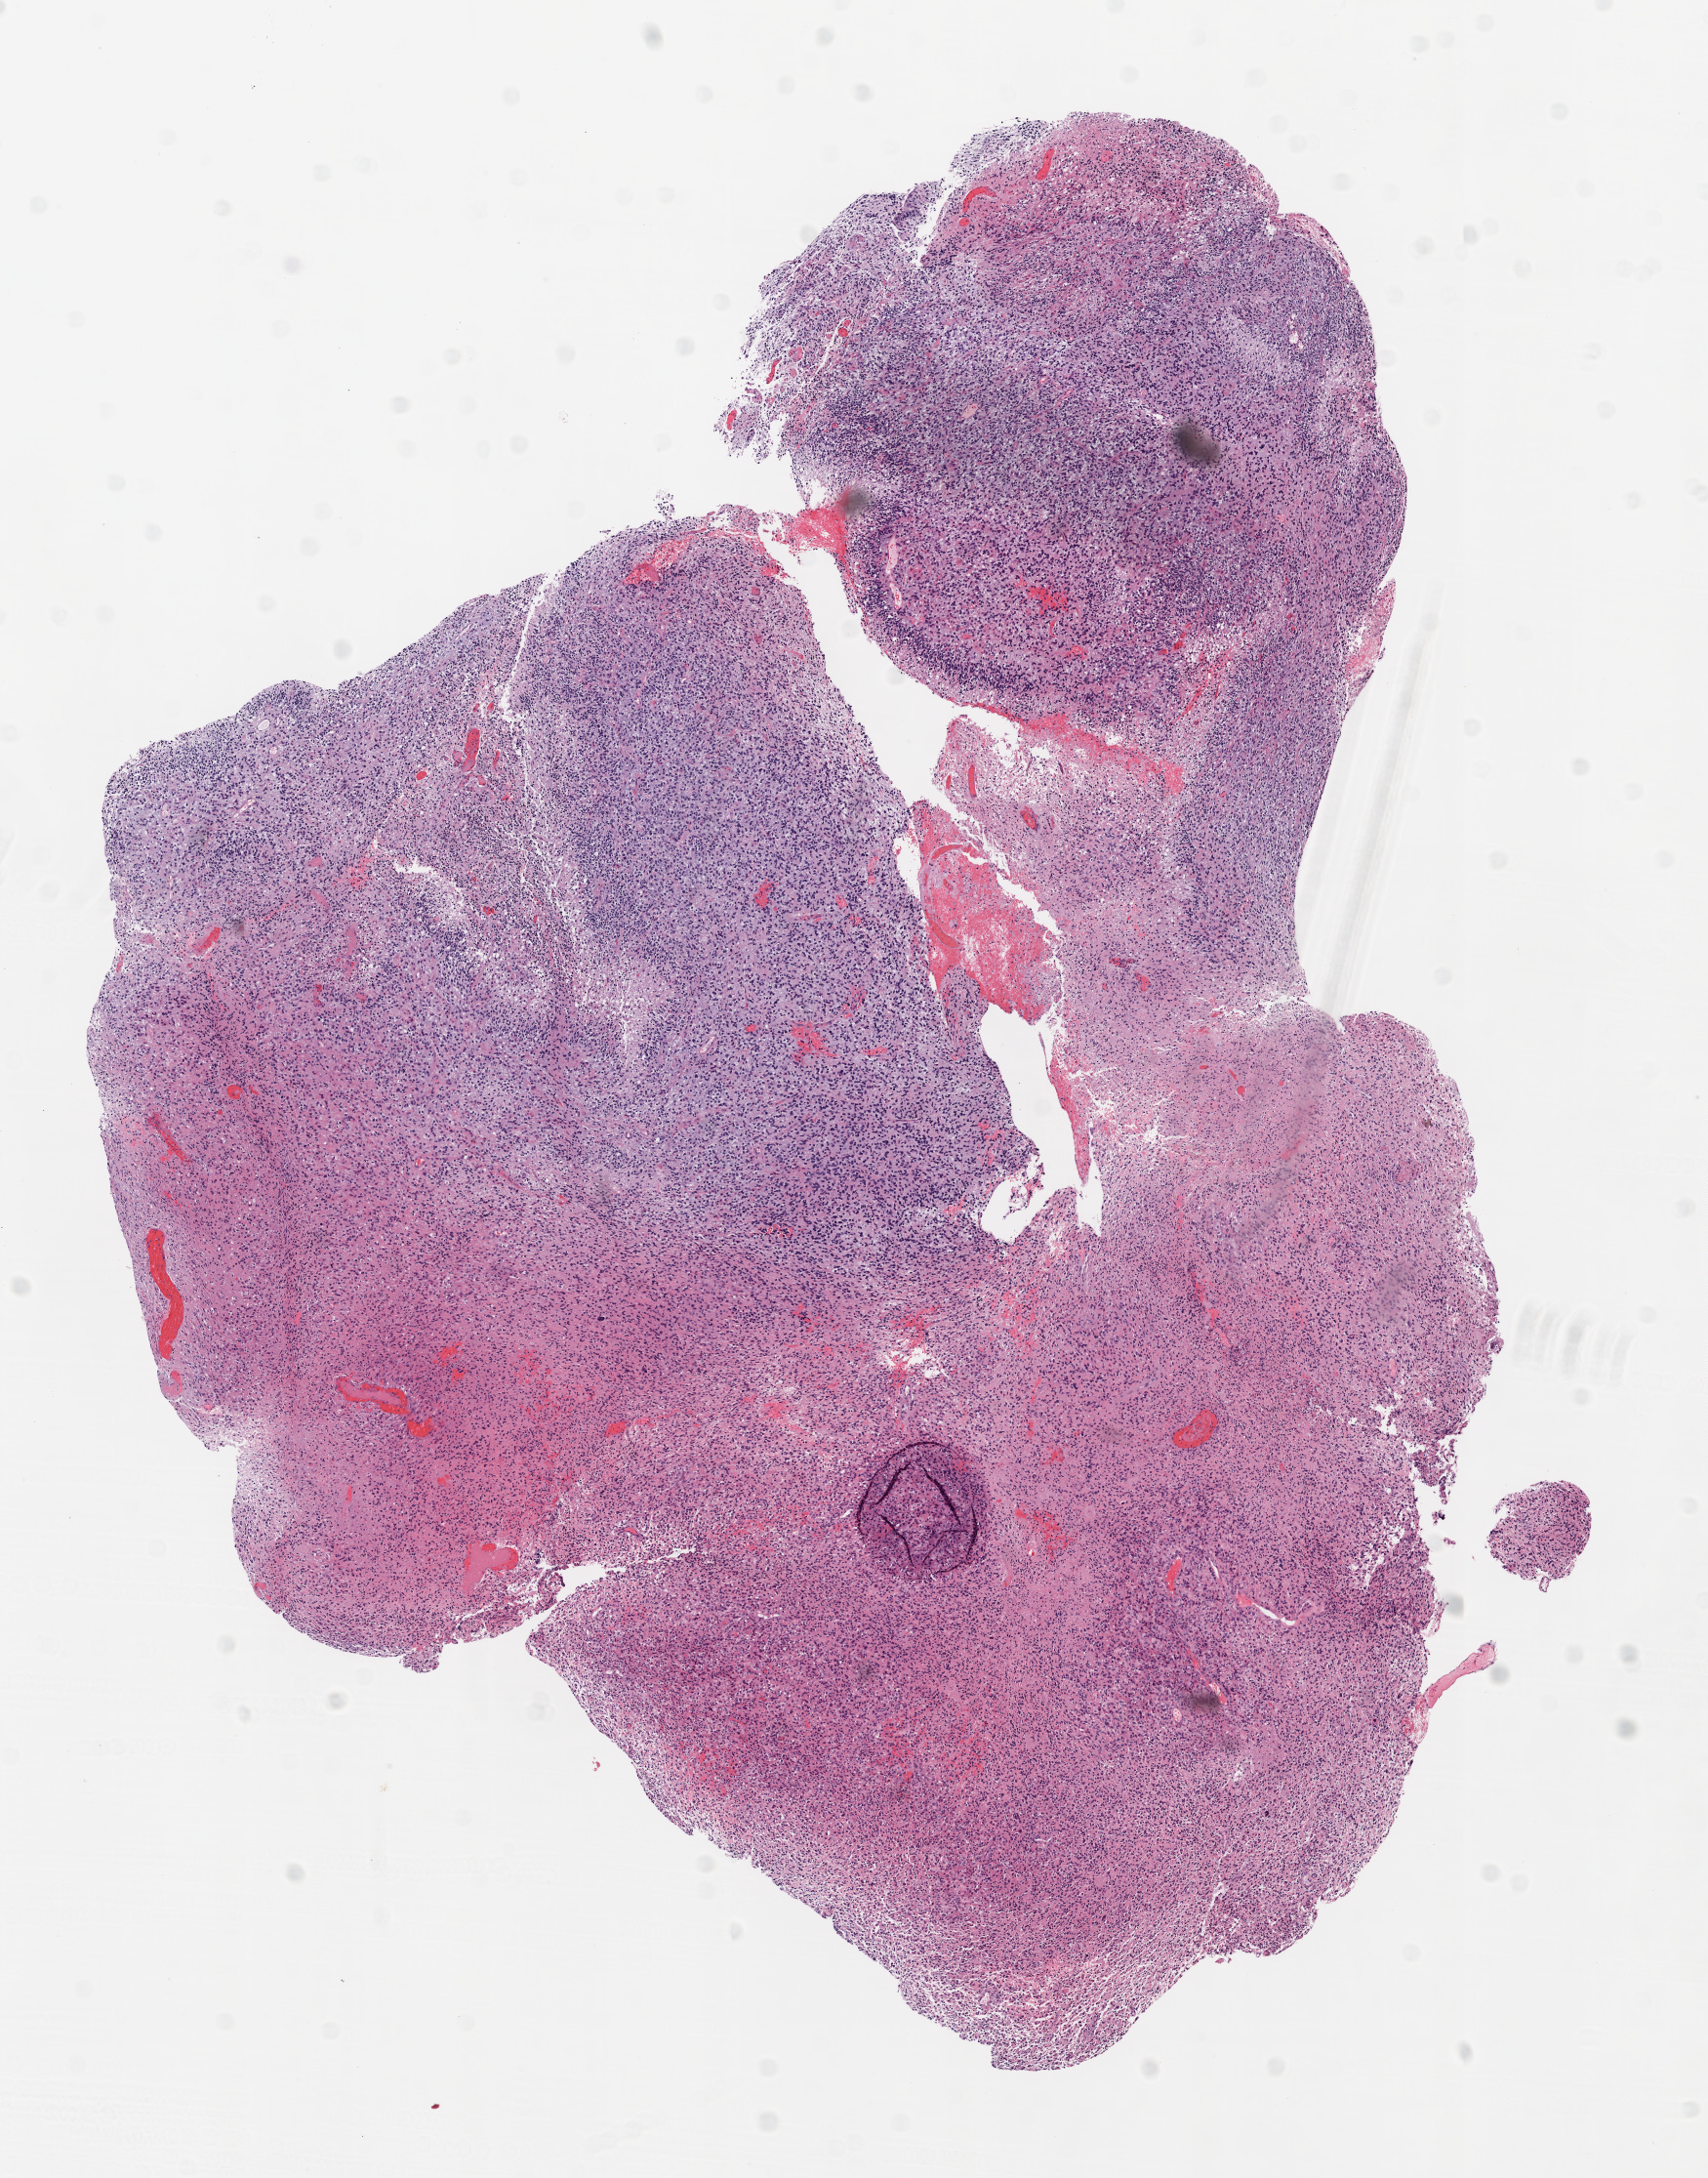
Digitized Hematoxylin and eosin (H&E) stained tissue section (whole slide), shown as a low-resolution overview of the whole scanned area (about 7.0 x 9.0 mm); FFPE section; brain, primary tumour sample. Female patient; age at initial diagnosis 63 years.
Diagnosis: Glioblastoma.